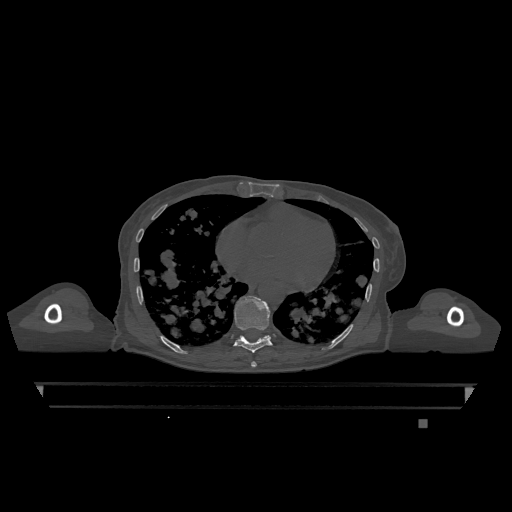
CT including the spine, one axial slice; slice 685 of 1317 in the series (ordered by position); bone window (W 1800 / L 400 HU); 0.5 mm slice thickness; 512 × 512 image matrix, field of view 500 × 500 mm. Patient: female, 74 years. From the clinical record (not read from this slice): primary cancer: lung.
Annotated regions visible in this slice (semi-automatic segmentation, software-assisted and operator-edited):
- T10 vertebra: box from (x=263, y=336) to (x=269, y=339) px
- T7 vertebra: (x=251, y=361)–(x=257, y=368)
- T9 vertebra: (x=234, y=296)–(x=273, y=353)